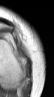
MRI of an extremity soft-tissue mass, one axial slice; position 14 of 42 along the scan axis; MR volume resampled by the dataset authors to the PET/CT grid (not the native acquisition matrix); 3.27 mm slice thickness; 54 × 97 image matrix, field of view 53 × 95 mm. Female patient. Case-level facts recorded for this patient, not image findings: histological type: spindle cell suggestive of biphasic synovial sarcoma; grade: intermediate; site of the primary tumour: left knee.
Annotated regions visible in this slice (expert contour drawn on MRI and transferred to this co-registered scan by the dataset authors):
- gross tumour volume including surrounding oedema: bounding box [x1, y1, x2, y2] px = [17, 48, 29, 70]
- gross tumour volume (mass): [17, 48, 29, 68]